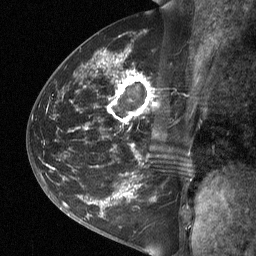
Breast MRI (dynamic contrast-enhanced), one sagittal slice. Dynamic contrast-enhanced study with each time point stored as its own series, time point 2 of 3 at this slice position (early post-contrast, ordered by acquisition time). 1.5 T. TE 4.8 ms, TR 27 ms. 2 mm slice thickness. 256 × 256 image matrix, field of view 200 × 200 mm. Patient: female, 42 years. From the clinical record (not read from this slice): setting: breast cancer imaged before/during neoadjuvant chemotherapy; receptor status: triple-negative.
Structures marked on this image (semi-automatically segmented with operator editing):
- analysis volume of interest (the breast-tissue region the enhancement analysis was run in; not a lesion): bounding box (x1, y1, x2, y2) in pixels: (49, 45, 197, 197)
- tumour enhancement mask (voxels above the 90 % enhancement threshold inside the analysis volume of interest): (115, 60, 148, 117)